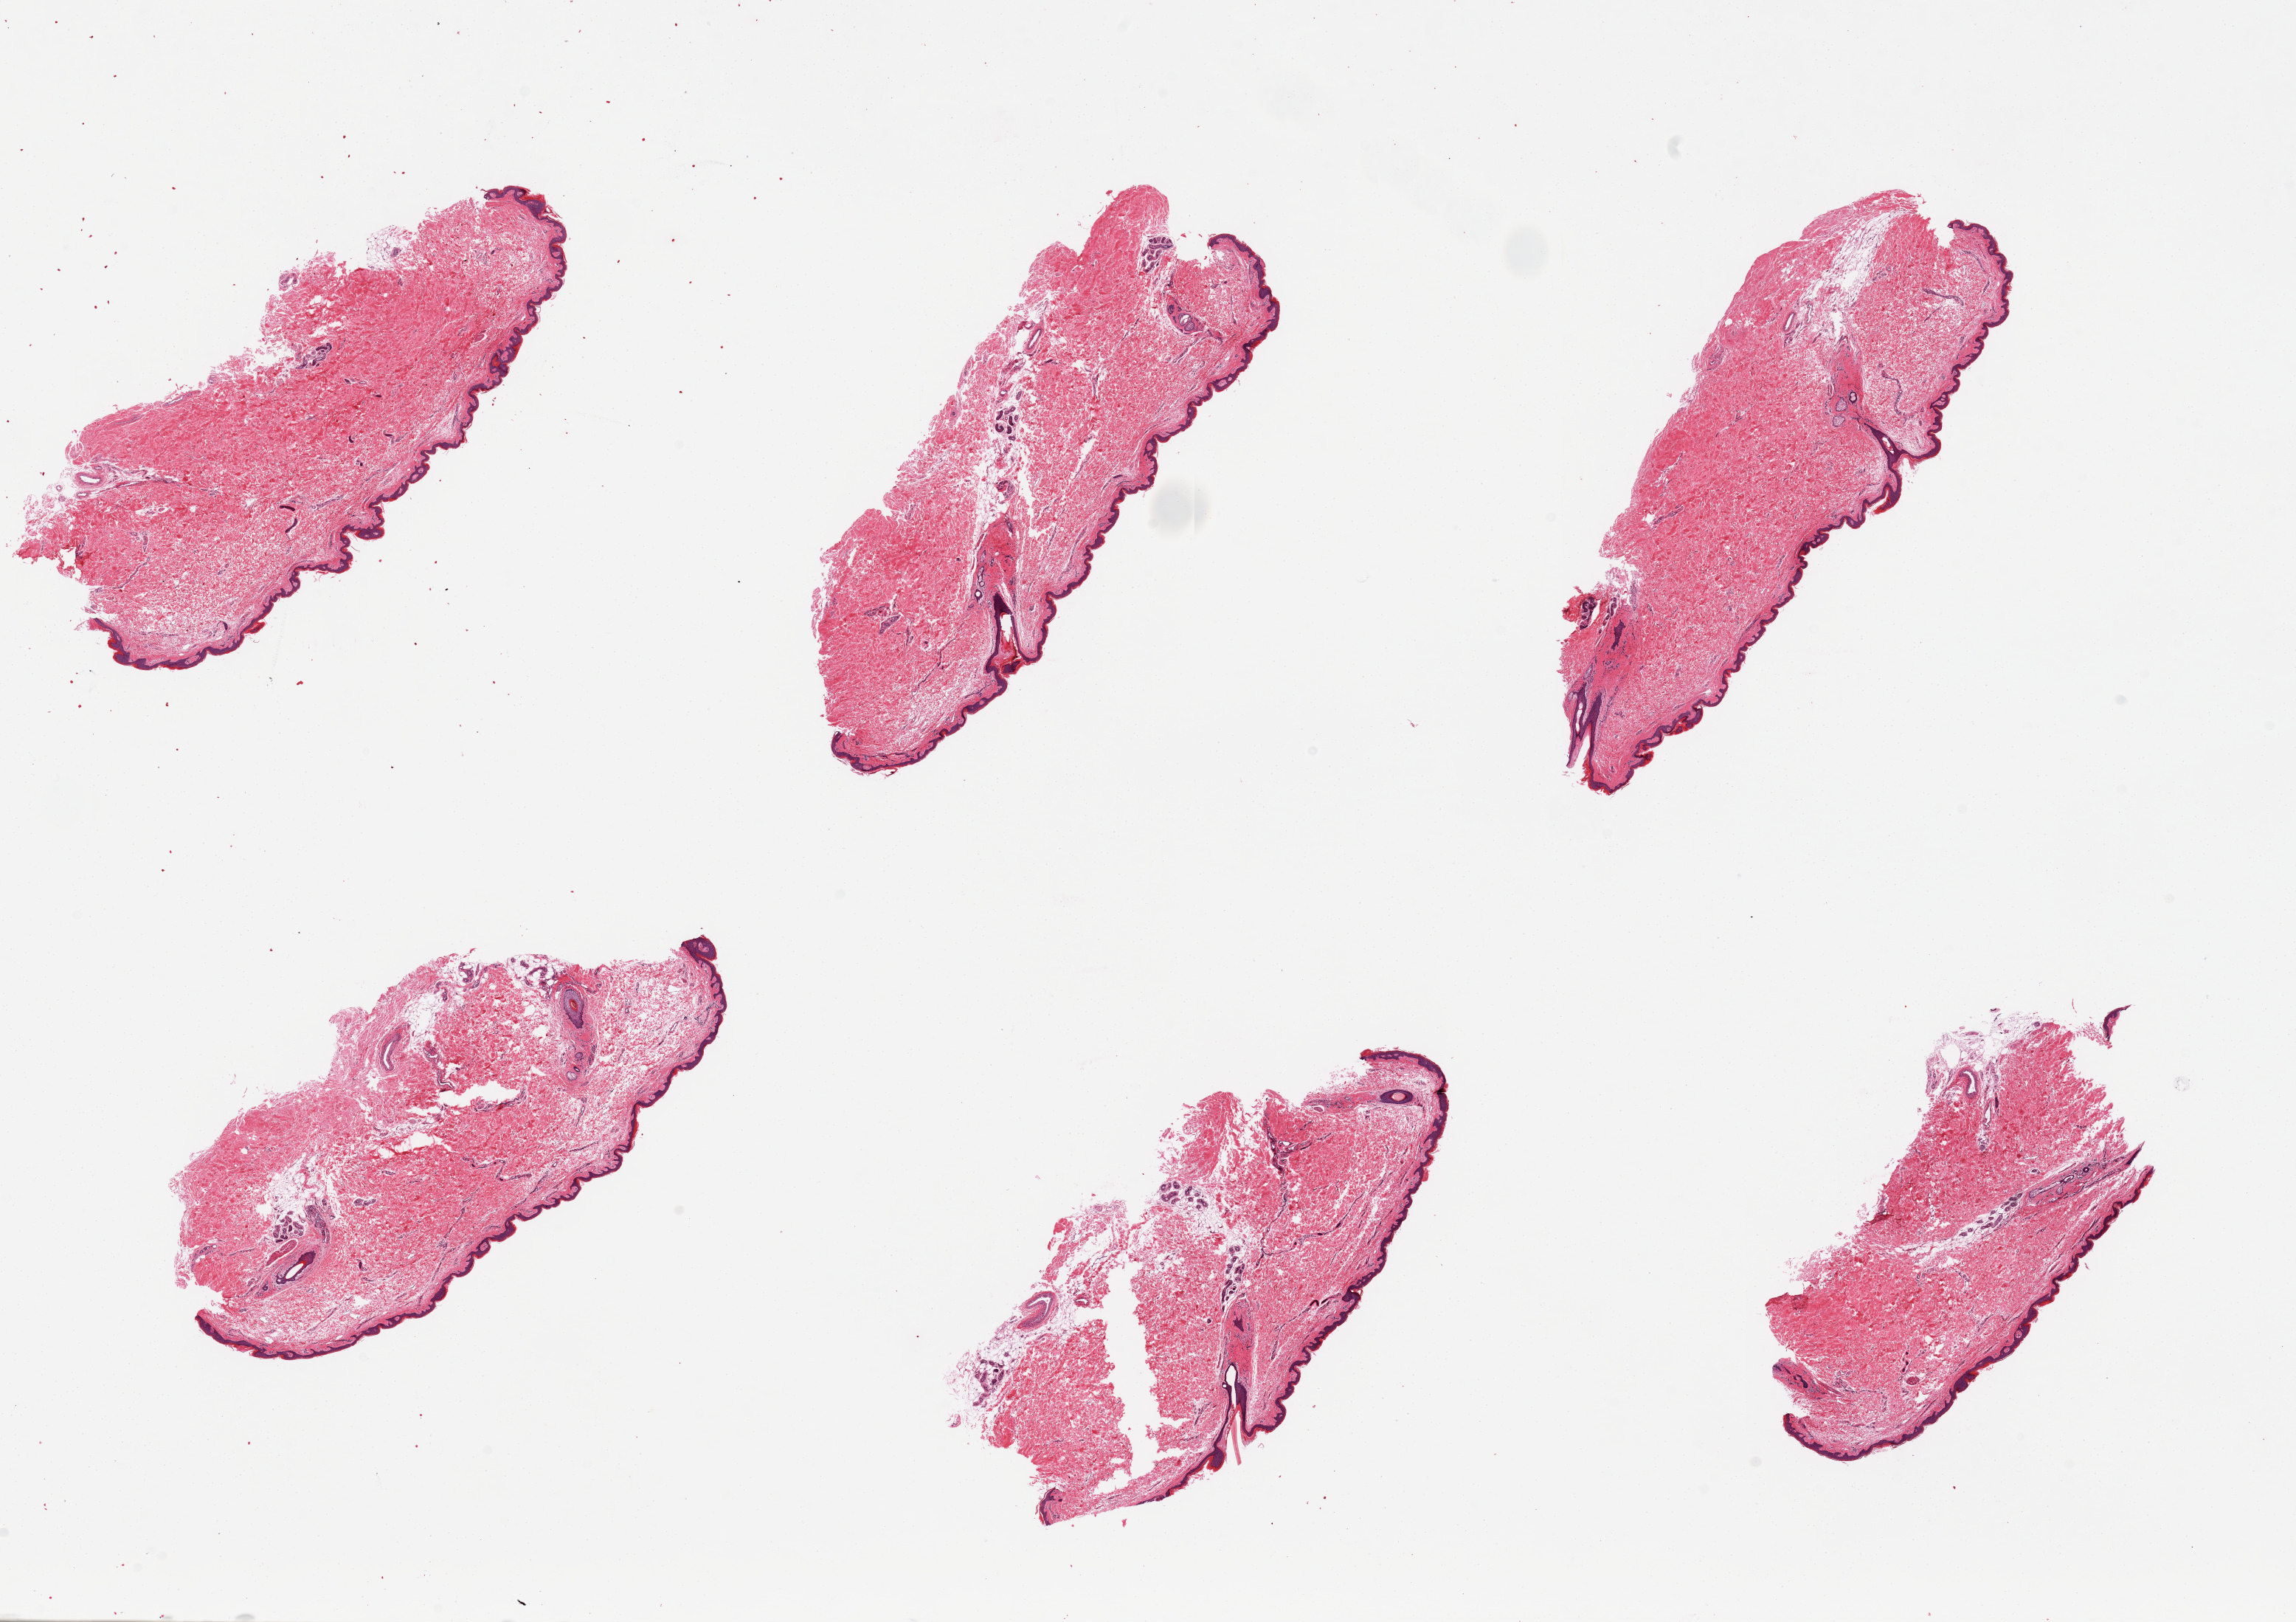
Hematoxylin and eosin (H&E) whole-slide image, brightfield — whole scanned area (about 24.6 x 17.4 mm, from a 20x scan) shown as a low-resolution overview, PAXgene-fixed paraffin-embedded (PFPE) section, target tissue: skin of suprapubic region, tissue donor sample.
* review note (as recorded): 6 pieces; <10% intradermal fat; well trimmed